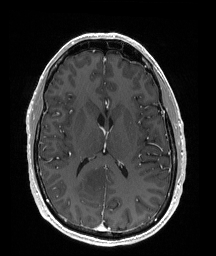
Brain MRI from a brain-tumour surgery series, one axial slice; slice 86 of 176 in the series (ordered by position); T1-weighted post-contrast; 1 mm slice thickness; 216 × 256 image matrix. From the clinical record (not read from this slice): histopathology: Oligodendroglioma; WHO grade: 2; IDH mutation: yes; tumour location: Right Parietal.
Structures marked on this image (outlined manually by an expert reader):
- tumour: bounding box (x1, y1, x2, y2) in pixels: (70, 163, 111, 202)